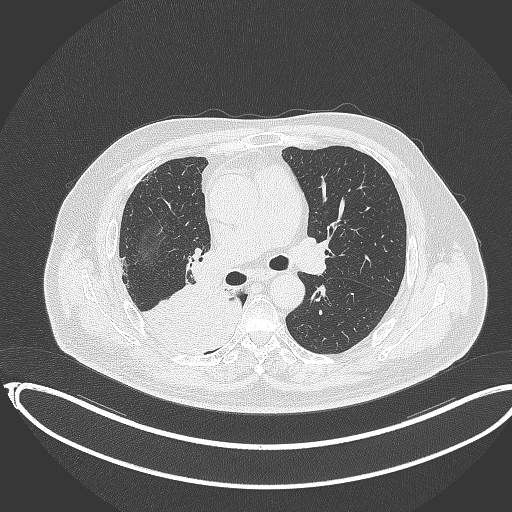
Chest CT, one axial slice. Position 209 of 403 along the scan axis. Reconstruction kernel B70f. Lung window (W 1500 / L -600 HU). 512 × 512 image matrix. Male patient, age 68 years. Case-level facts recorded for this patient, not image findings: clinical TNM (as recorded): T2a N0 M0.
Outlined on this slice (bounding box drawn by a radiologist):
- lung tumour (recorded histology: adenocarcinoma): box from (x=141, y=280) to (x=244, y=360) px